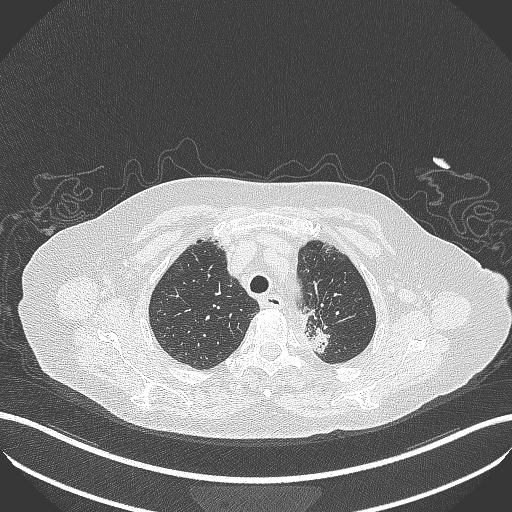
Chest CT, one axial slice; slice 278 of 353 in the series (ordered by position); 100 kVp; lung window (W 1500 / L -600 HU); 512 × 512 image matrix. Female patient, age 81 years. From the clinical record (not read from this slice): clinical TNM (as recorded): T2a N0 M0.
Annotated regions visible in this slice (bounding box drawn by a radiologist):
- lung tumour (recorded histology: adenocarcinoma): box from (x=295, y=302) to (x=339, y=359) px